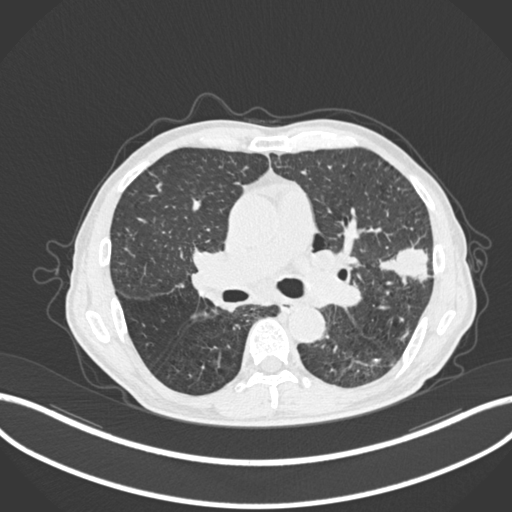
Chest CT, one axial slice; position 143 of 287 along the scan axis; reconstruction kernel B30f; 120 kVp; lung window (W 1500 / L -600 HU); 1 mm slice thickness; 512 × 512 image matrix, field of view 400 × 400 mm. Male patient, age 74 years. From the clinical record (not read from this slice): clinical TNM (as recorded): T2a N1 M0.
Annotated regions visible in this slice (rectangle marked by the reading radiologist):
- lung tumour (recorded histology: adenocarcinoma): bounding box [x1, y1, x2, y2] px = [377, 246, 432, 285]